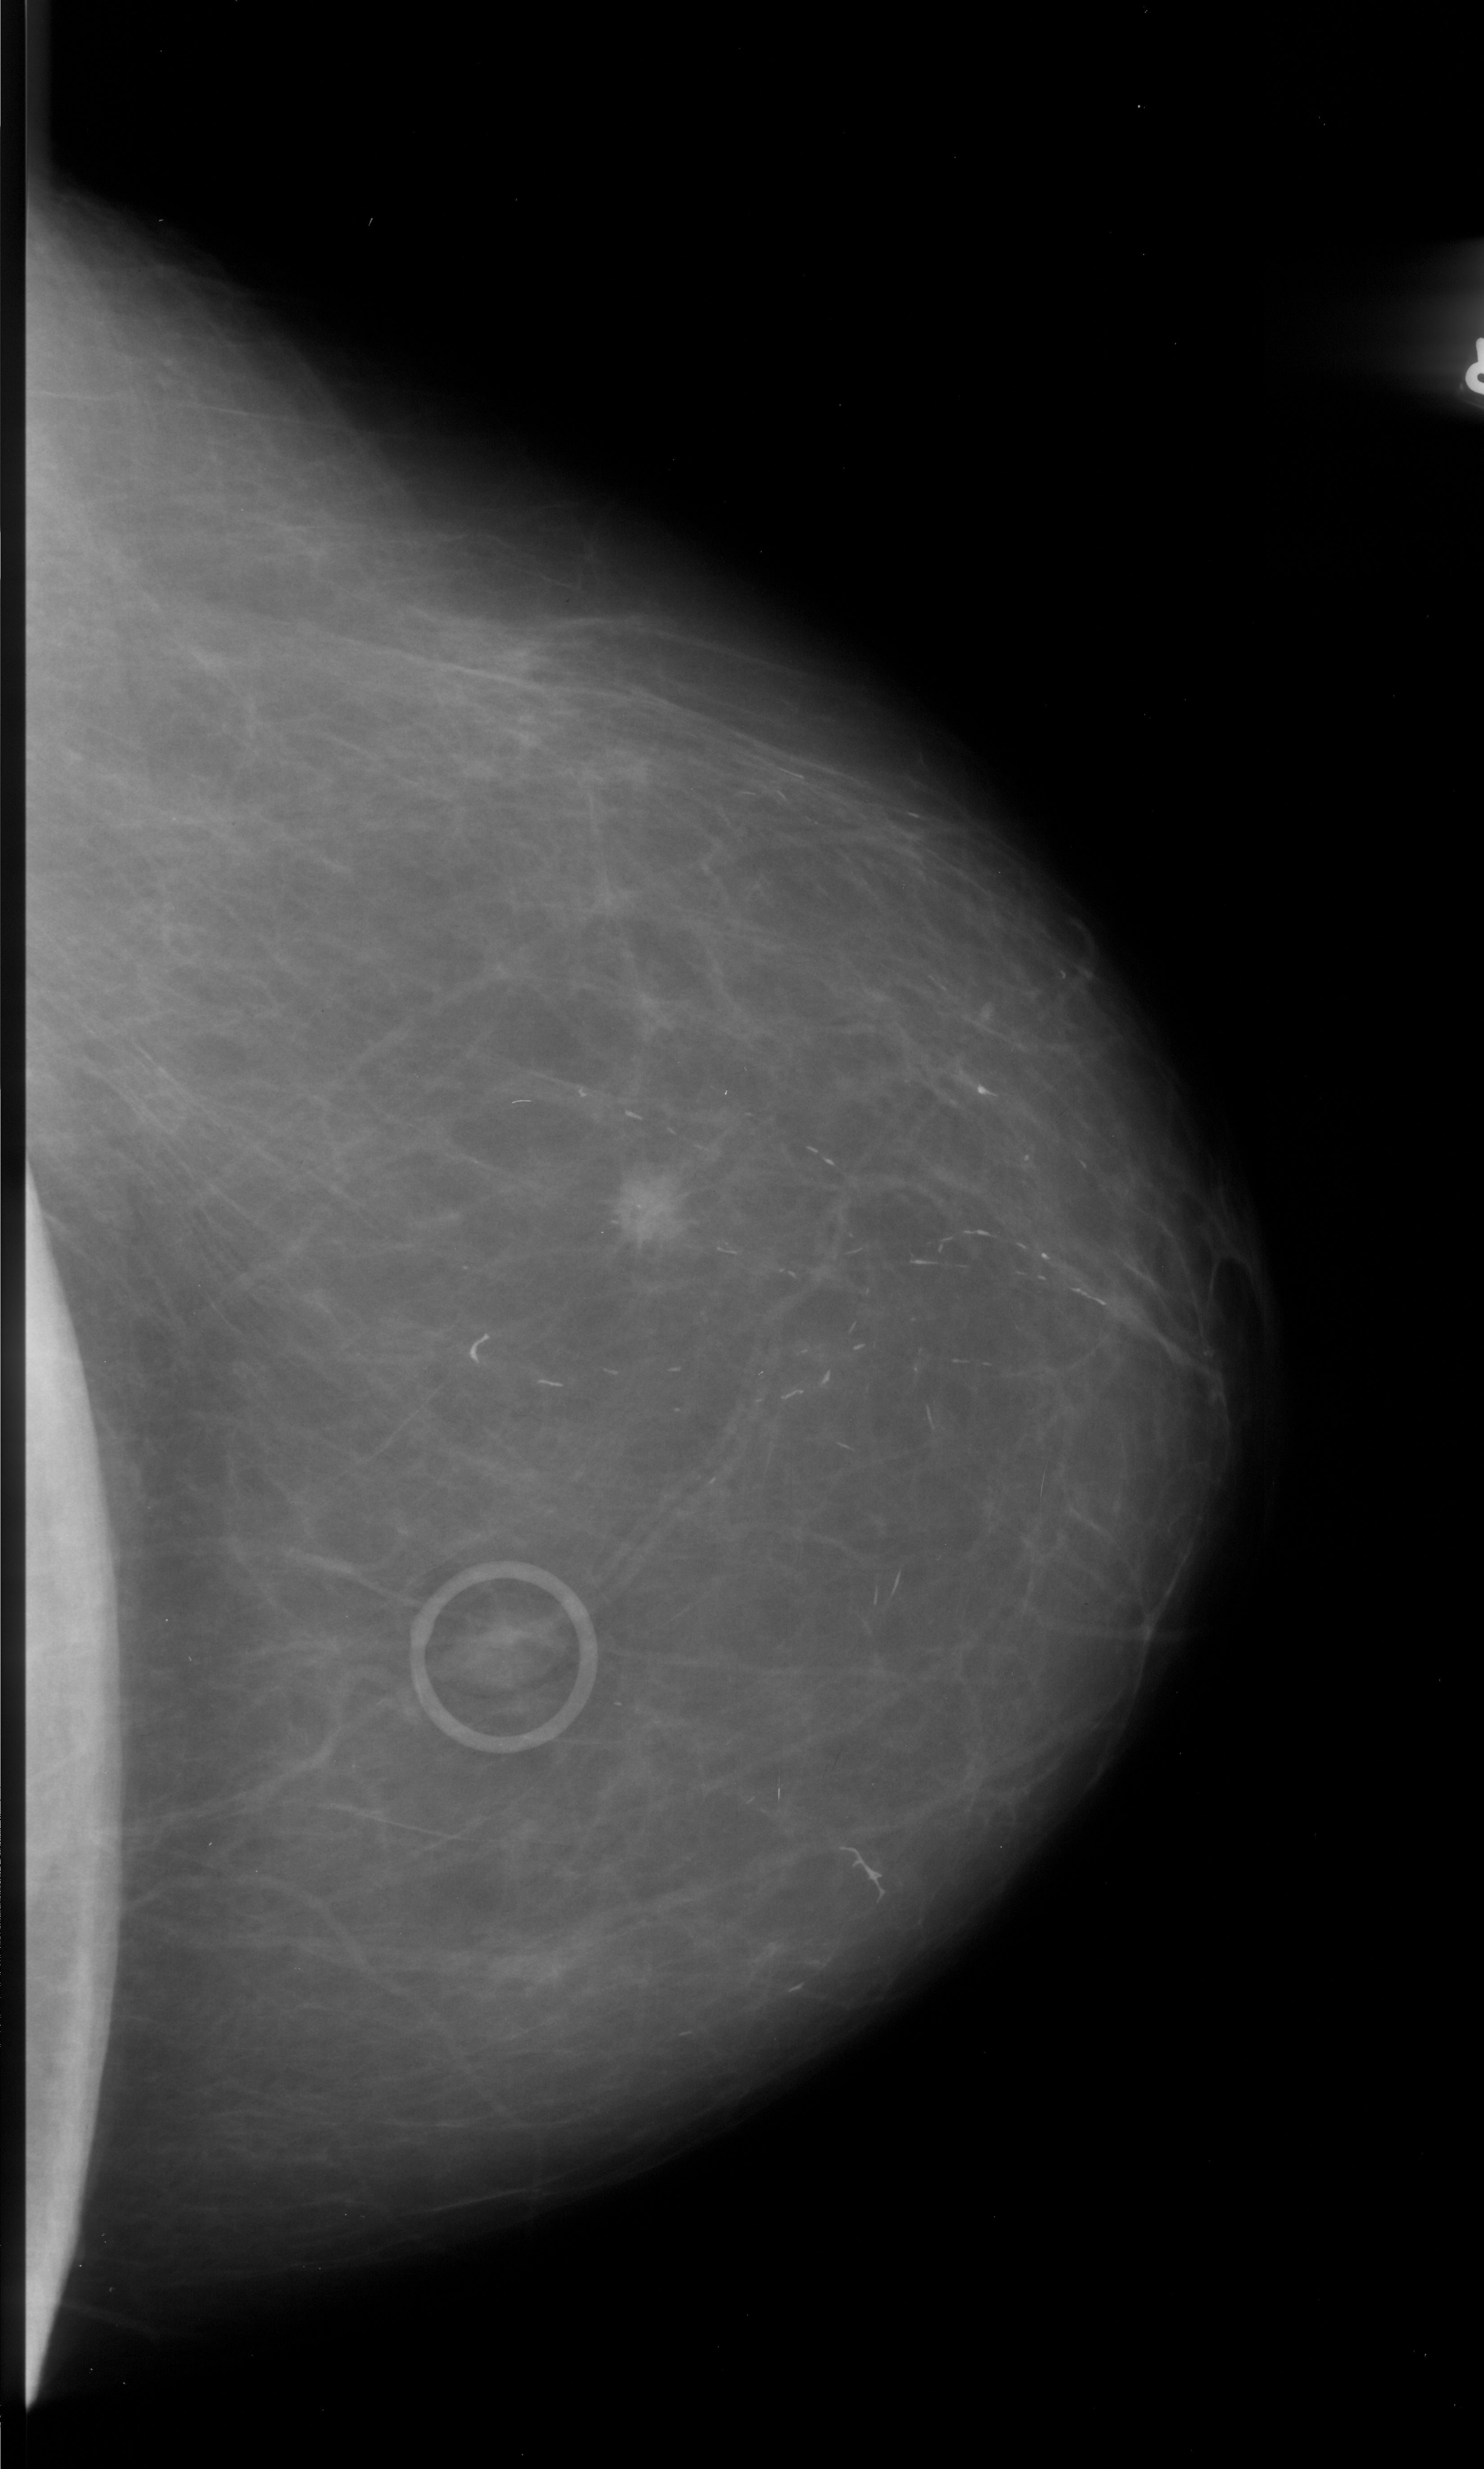
Digitized screen-film mammogram. Right breast. CC view. Breast composition: almost entirely fatty (BI-RADS density category 1 of 4). 1484 × 2469 image matrix.
Marked abnormalities (boxes around the expert regions of interest):
- mass, shape irregular, margins spiculated; BI-RADS assessment category 5; subtlety rating 4 on a 1 (subtle) to 5 (obvious) scale; pathology (as recorded): malignant: bounding box <595,1157,696,1259> (left, top, right, bottom; pixels)